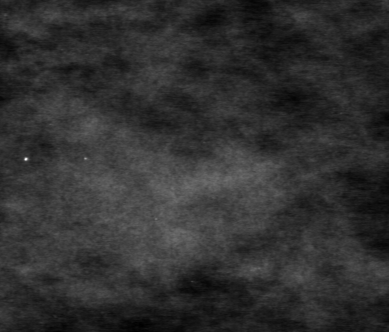
Cropped region of a digitized screen-film mammogram centred on a radiologist-marked abnormality; left breast; MLO view; BI-RADS breast density category 1 (scale 1–4).
Mass, shape lobulated, margins obscured; BI-RADS assessment category 0 (incomplete: needs additional imaging); pathology result (as recorded, not read from the image): benign.